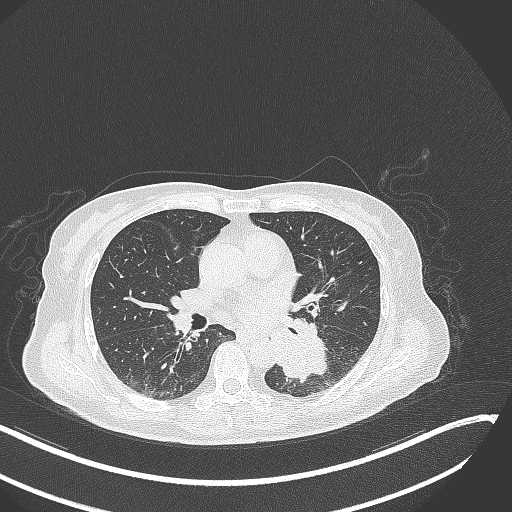
Chest CT, one axial slice. Position 141 of 342 along the scan axis. Reconstruction kernel B70f. Lung window (W 1500 / L -600 HU). 512 × 512 image matrix, field of view 400 × 400 mm. Patient: female, 64 years. Case-level facts recorded for this patient, not image findings: clinical TNM (as recorded): T3 N1 M1; histopathological grade: G3.
Outlined on this slice (rectangle marked by the reading radiologist):
- lung tumour (recorded histology: small cell carcinoma): bounding box <267,326,336,386> (left, top, right, bottom; pixels)